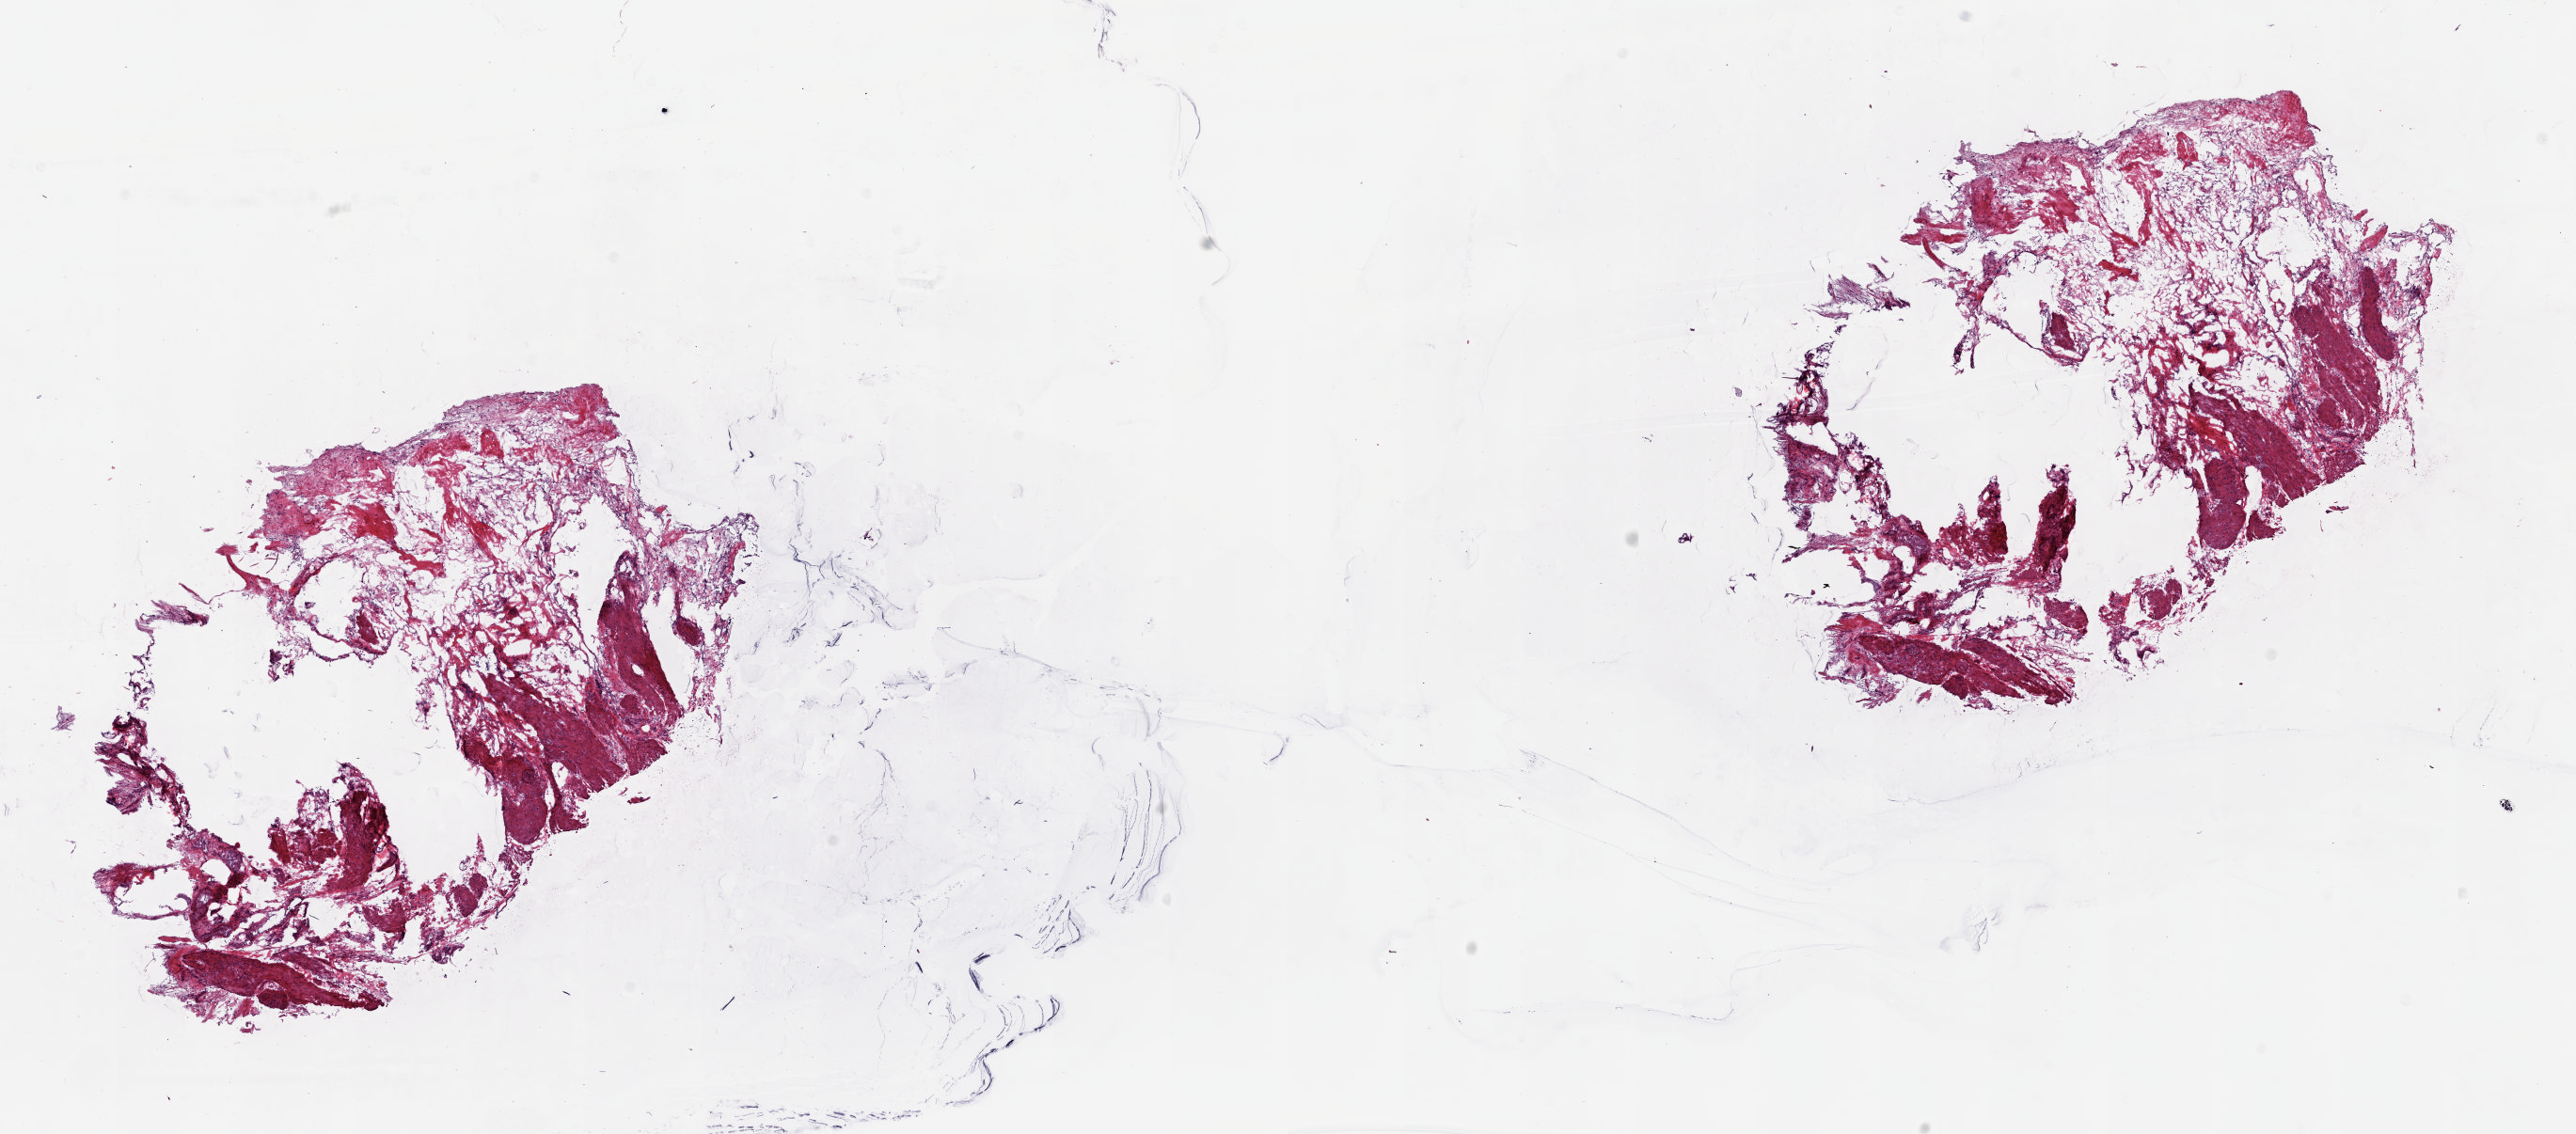
Digitized Hematoxylin and eosin (H&E) stained tissue section (whole slide), whole scanned area (about 21.8 x 9.6 mm) shown as a low-resolution overview, frozen section from the top of the tissue portion, bladder, solid tissue normal (non-tumour tissue) sample. Patient: female, age at initial diagnosis 79 years. Composition of this section per pathologist review: tumour cells 0%, tumour nuclei 0%, normal cells 100%, stromal cells 0%, necrosis 0%. Infiltration values recorded for this section: lymphocyte infiltration 0%, monocyte infiltration 0%, neutrophil infiltration 0%.
This section: solid tissue normal sample (biorepository sample class). Patient diagnosis: Transitional cell carcinoma (trigone of bladder).